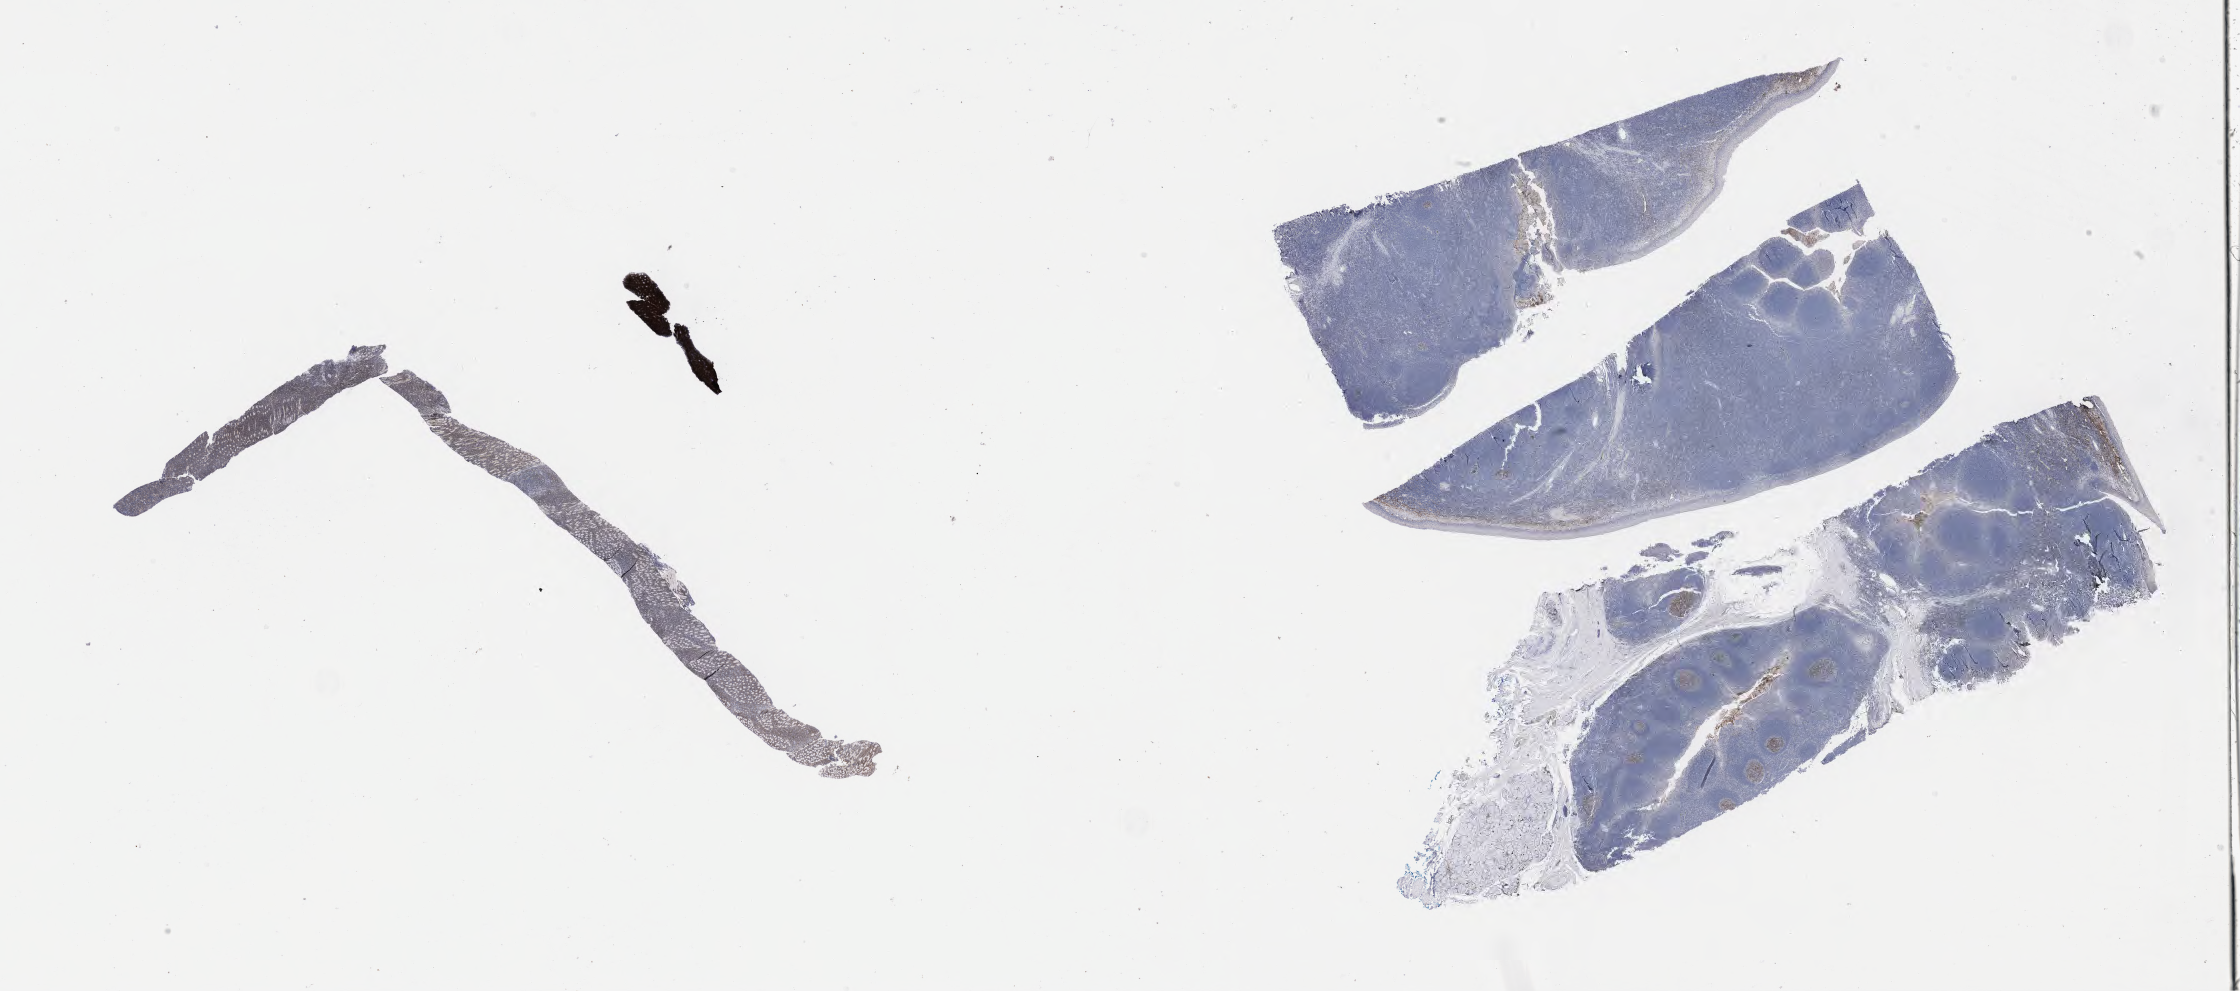
IHC for CD10, whole-slide image, shown as a low-resolution overview of the whole scanned area (about 36.2 x 16.0 mm), tumor tissue. Male patient; age at initial diagnosis 4 years.
Diagnosis: Burkitt lymphoma, NOS.